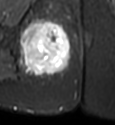
MRI of an extremity soft-tissue mass, one axial slice; slice 24 of 49 in the series (ordered by position); STIR; MR volume resampled by the dataset authors to the PET/CT grid (not the native acquisition matrix); 3.27 mm slice thickness; 115 × 125 image matrix, field of view 112 × 122 mm. Female patient. From the clinical record (not read from this slice): histological type: epithelioid sarcoma; grade: intermediate; site of the primary tumour: right buttock.
Outlined on this slice (expert contour drawn on MRI and transferred to this co-registered scan by the dataset authors):
- gross tumour volume including surrounding oedema: bounding box (x1, y1, x2, y2) in pixels: (19, 16, 71, 76)
- gross tumour volume (mass): (22, 21, 71, 72)